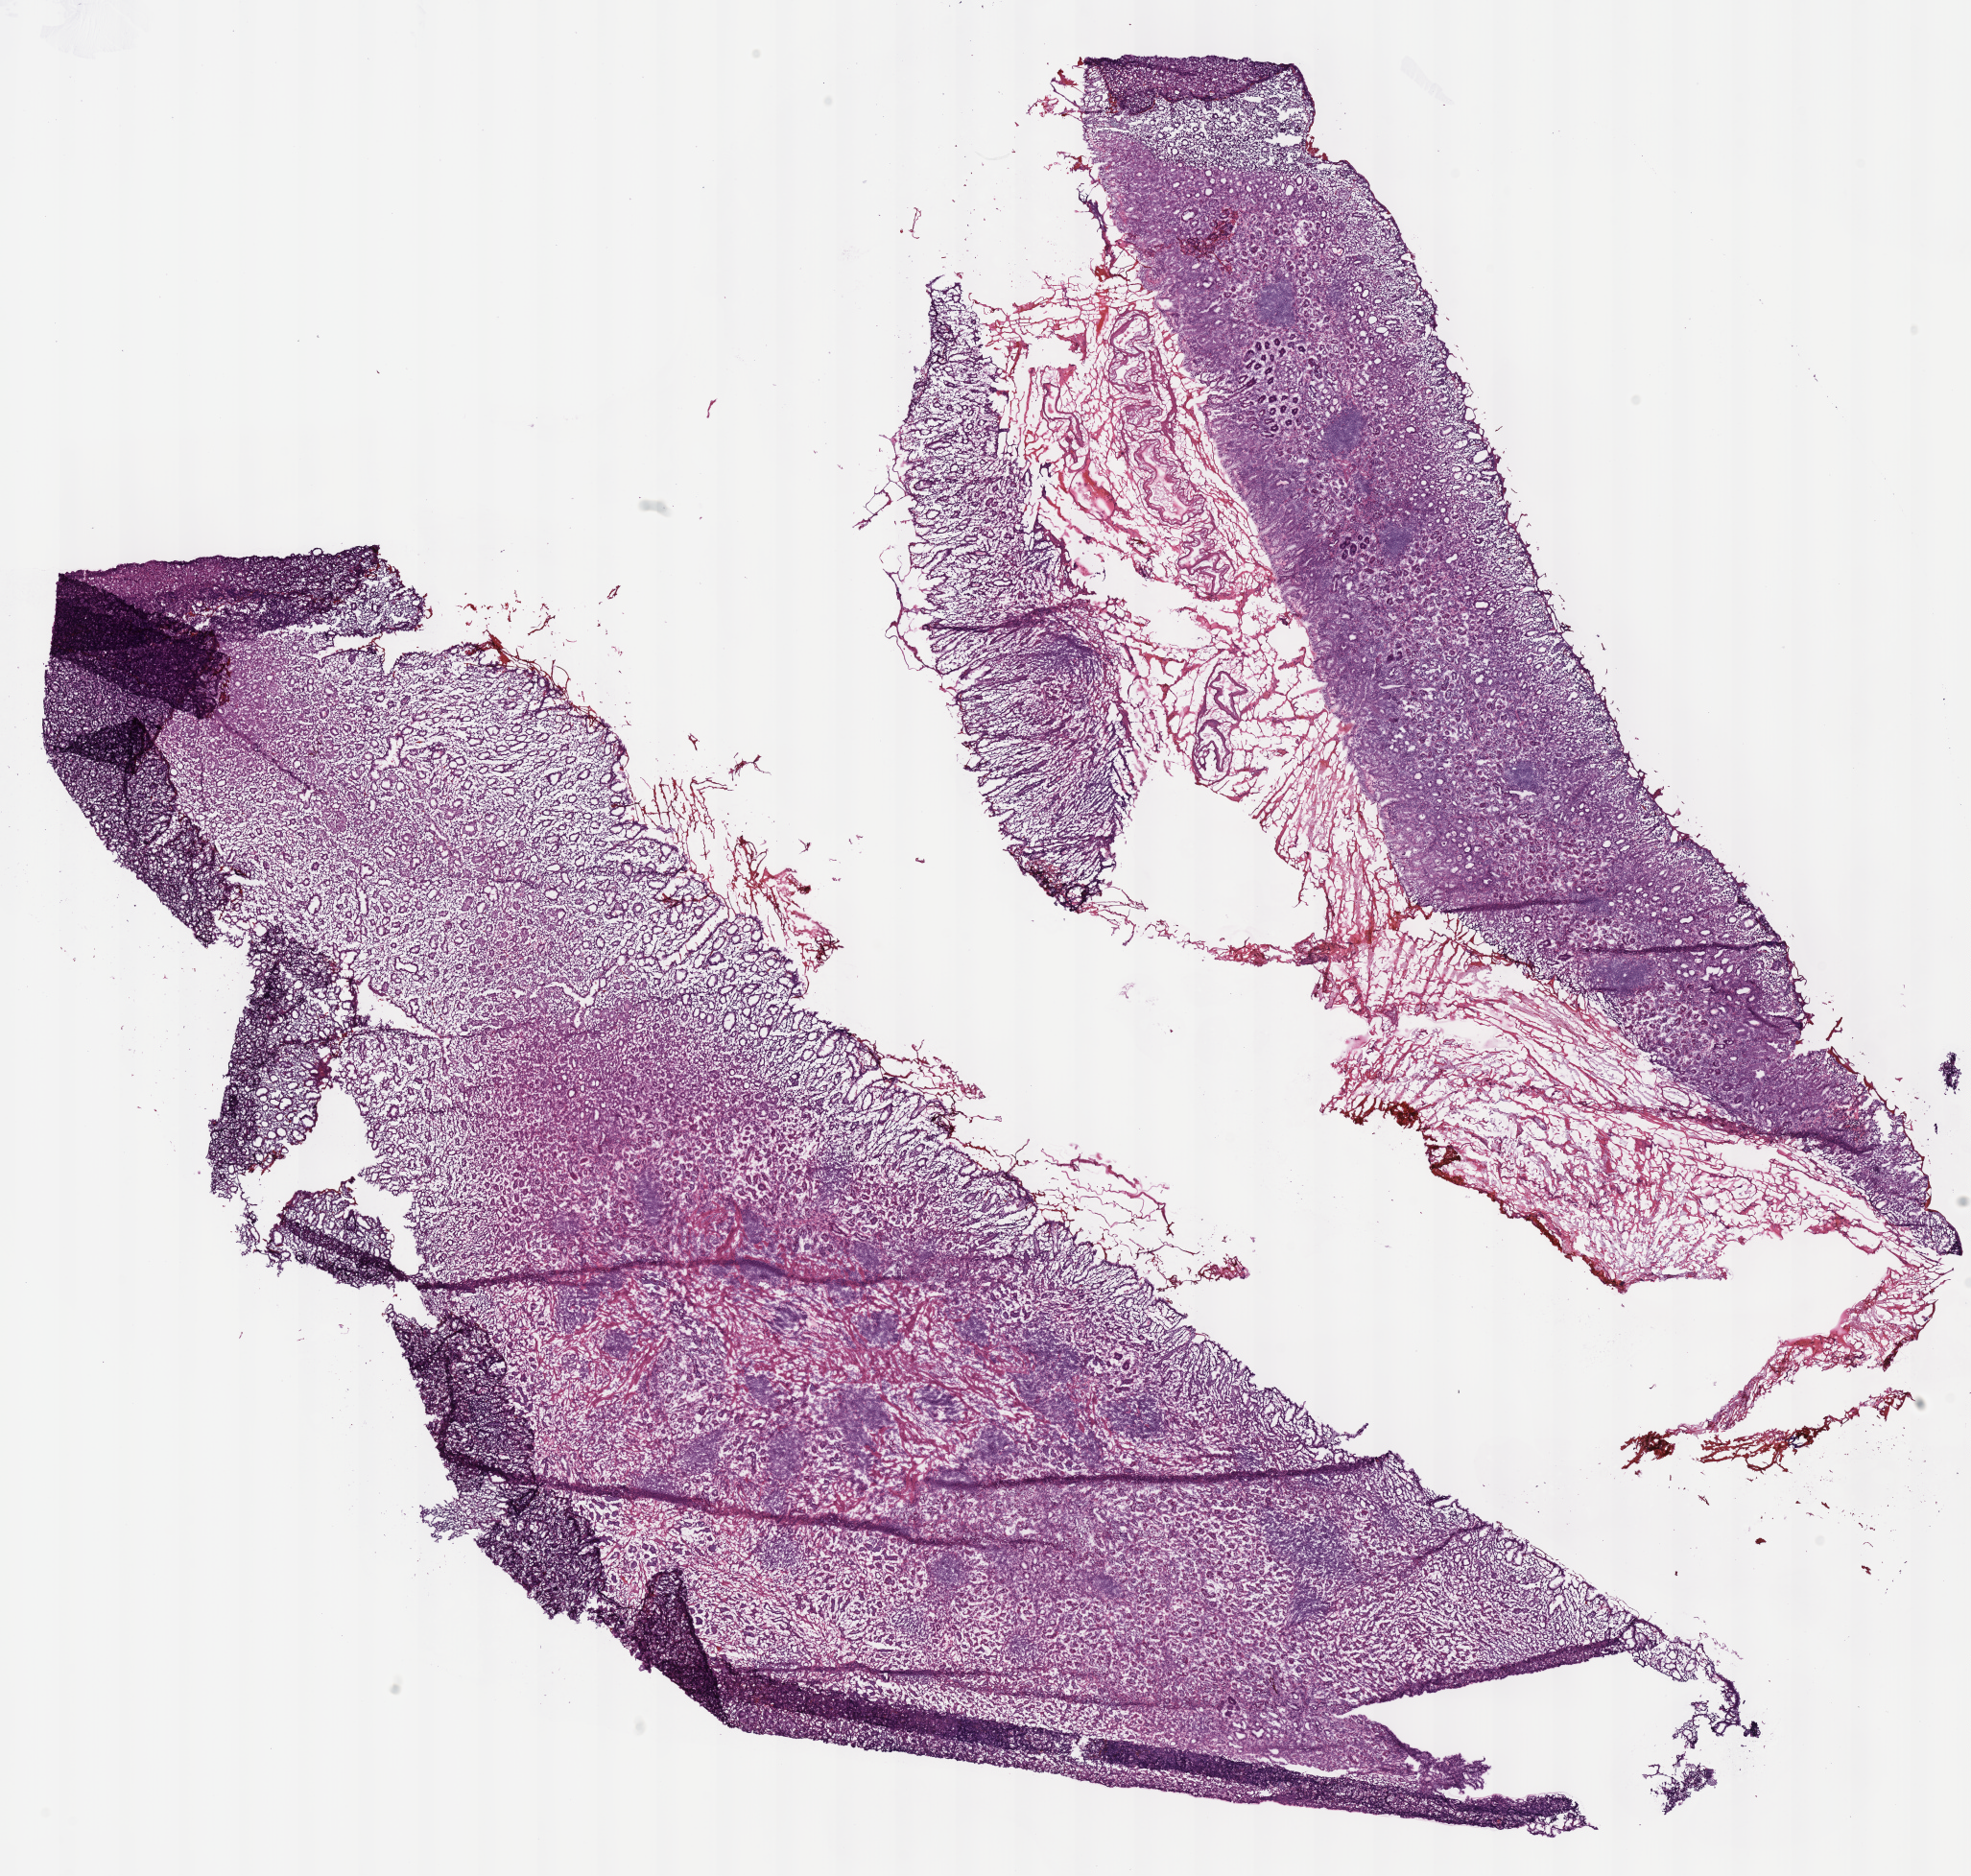
Digitized Hematoxylin and eosin (H&E) stained tissue section (whole slide) — whole scanned area (about 16.2 x 15.4 mm) shown as a low-resolution overview; frozen section from the top of the tissue portion; solid tissue normal (non-tumour tissue) sample from the stomach. Patient: male, age at initial diagnosis 65 years. Inflammatory infiltration, as recorded: lymphocyte infiltration 30%, monocyte infiltration 0%, neutrophil infiltration 5%.
- this section: solid tissue normal sample (biorepository sample class)
- patient diagnosis: Adenocarcinoma, NOS (body of stomach)